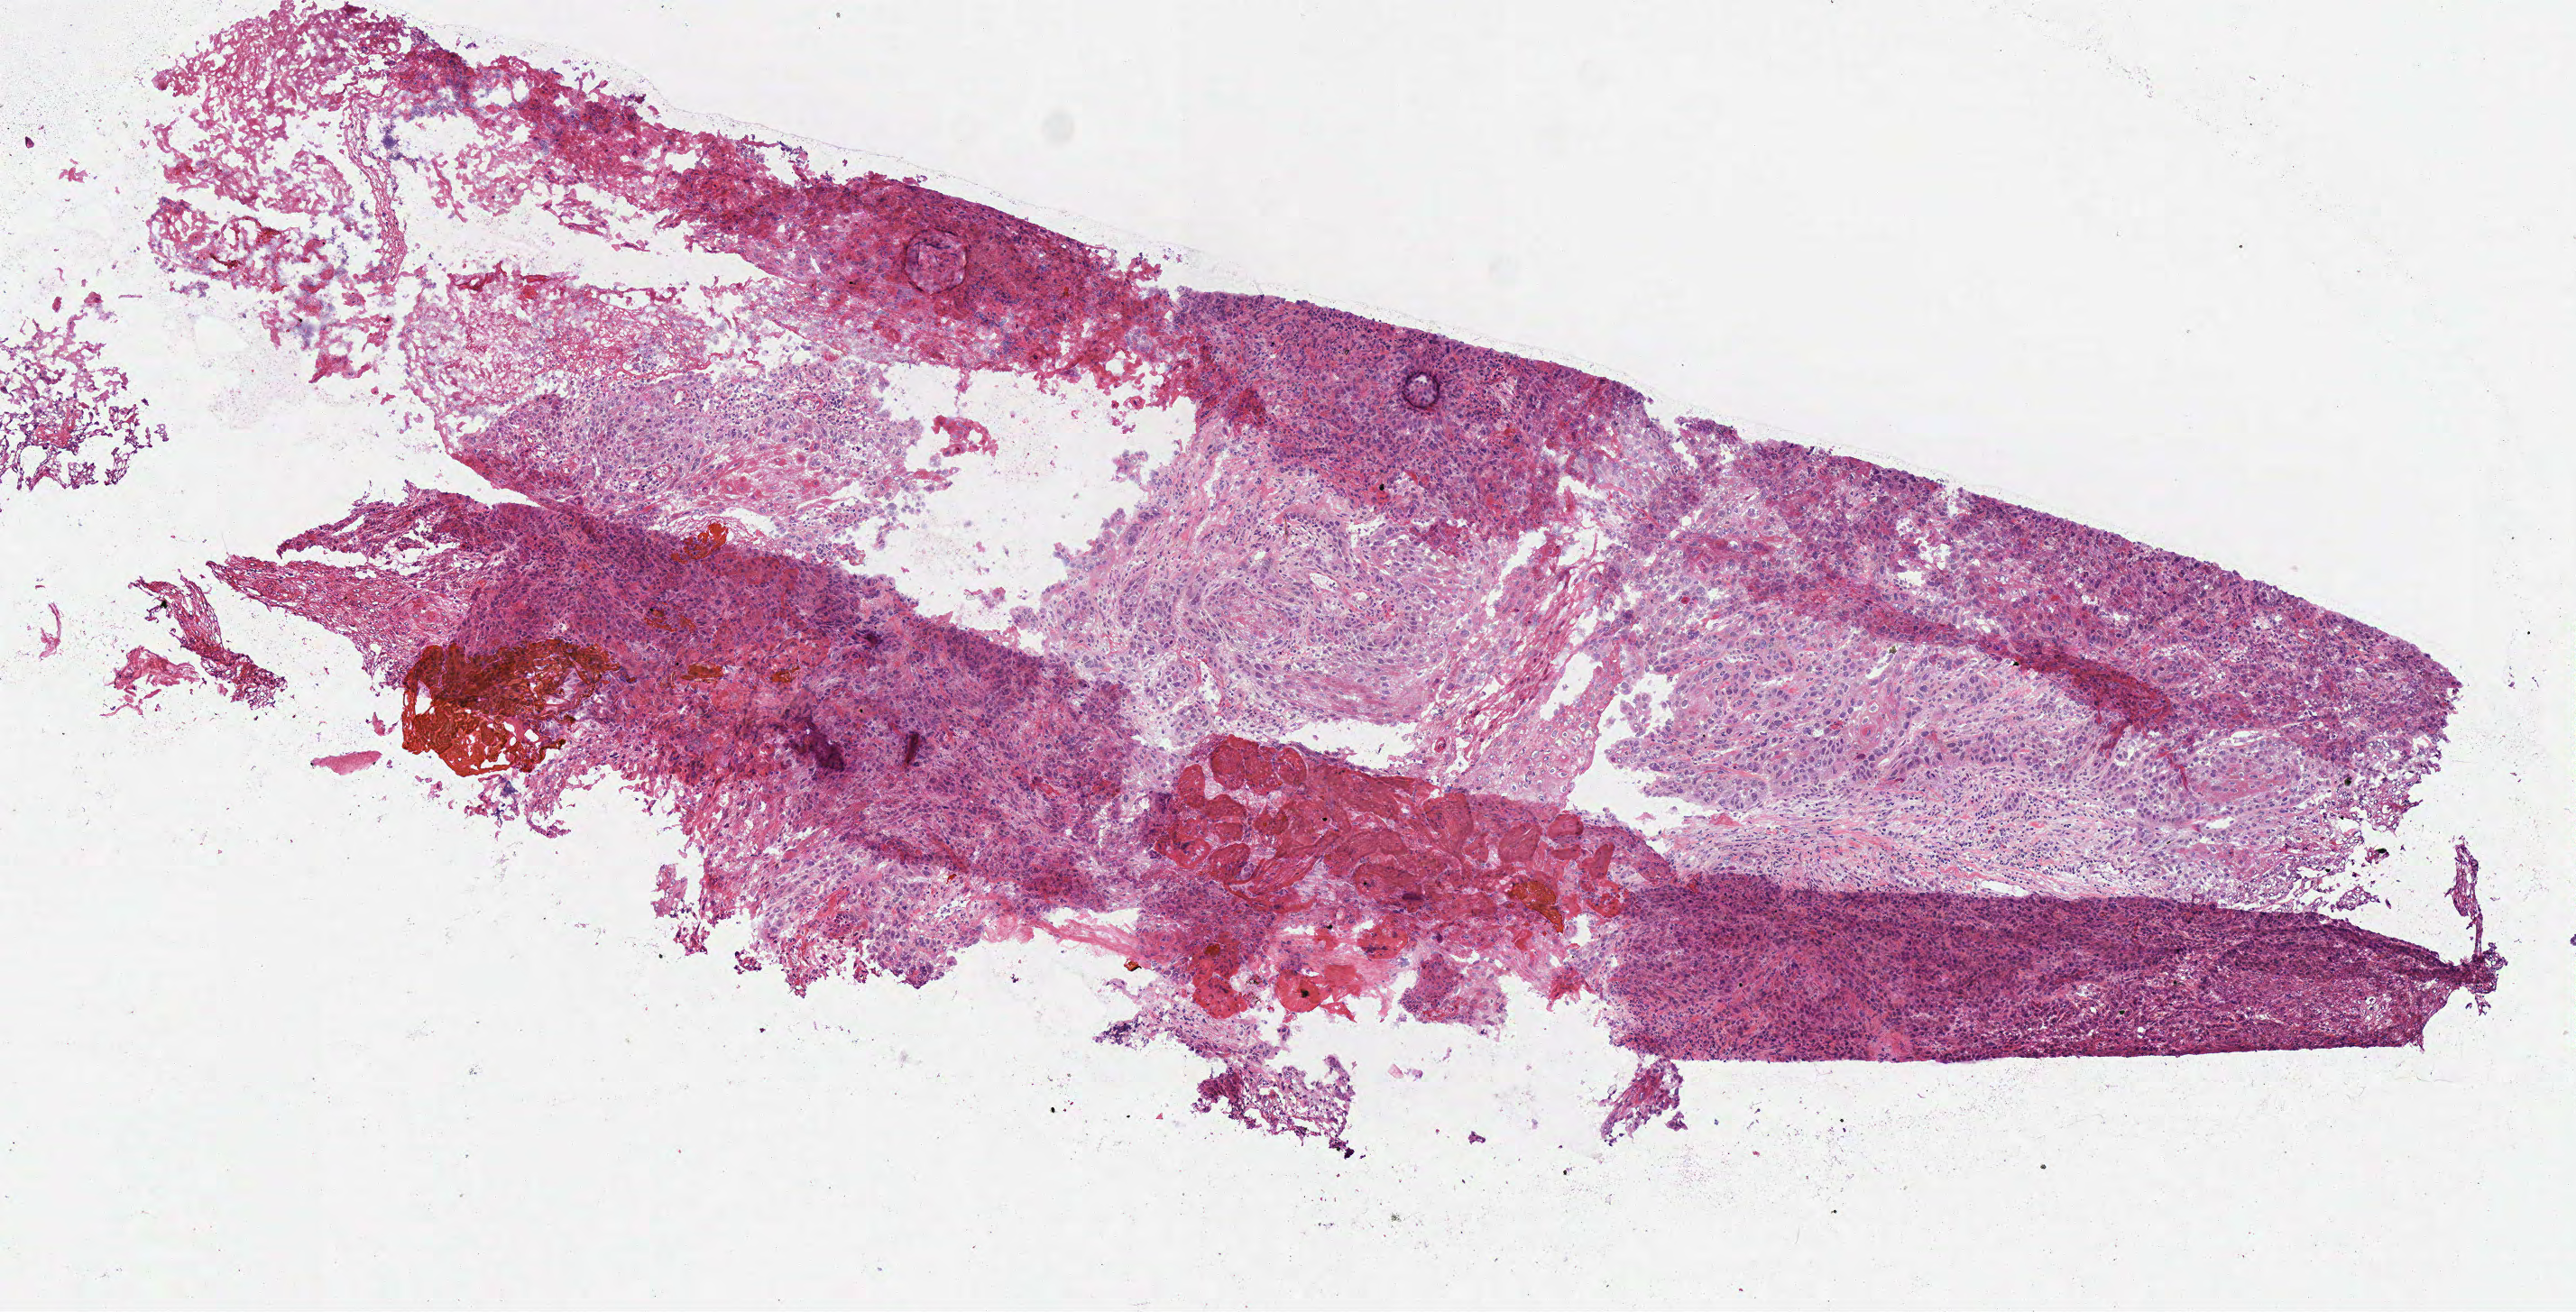
Digitized Hematoxylin and eosin (H&E) stained tissue section (whole slide), whole scanned area (about 5.6 x 2.9 mm, acquisition: 40x scan) shown as a low-resolution overview; frozen section from the bottom of the tissue portion; primary tumour sample from the head and neck. Patient: male, age at initial diagnosis 47 years. Histologic grade: G2 (moderately differentiated). Slide review estimates, as recorded: tumour cells 90%, tumour nuclei 95%, normal cells 0%, stromal cells 8%, necrosis 2%. Inflammatory infiltration, as recorded: lymphocyte infiltration 2%.
- diagnosis: Squamous cell carcinoma, NOS (floor of mouth, NOS)